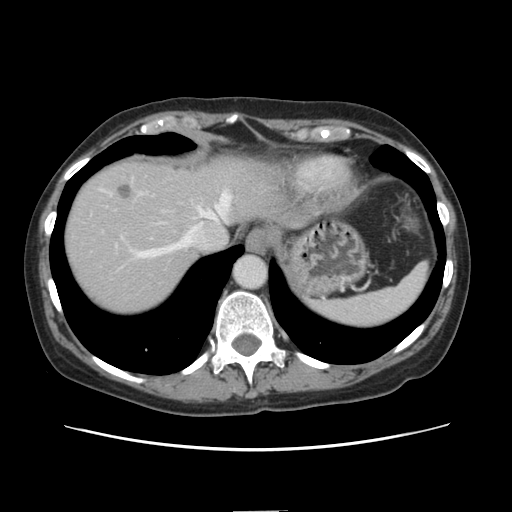
Contrast-enhanced abdominal CT, one axial slice. Slice 120 of 141 in the series (ordered by position). 120 kVp. Intravenous contrast given. Soft-tissue window (W 400 / L 40 HU). 512 × 512 image matrix, field of view 350 × 350 mm. Female patient, age 63 years. Case-level facts recorded for this patient, not image findings: diagnosis: colorectal cancer liver metastases, imaged before liver resection; multiple liver metastases: yes; largest metastasis: 3.2 cm.
Annotated regions visible in this slice (expert manual segmentation):
- hepatic veins: bounding box [x1, y1, x2, y2] px = [135, 193, 230, 259]
- liver: [64, 157, 296, 316]
- planned liver remnant (the part of the liver to remain after resection): [203, 156, 279, 227]
- portal vein (with intrahepatic branches): [203, 202, 219, 210]